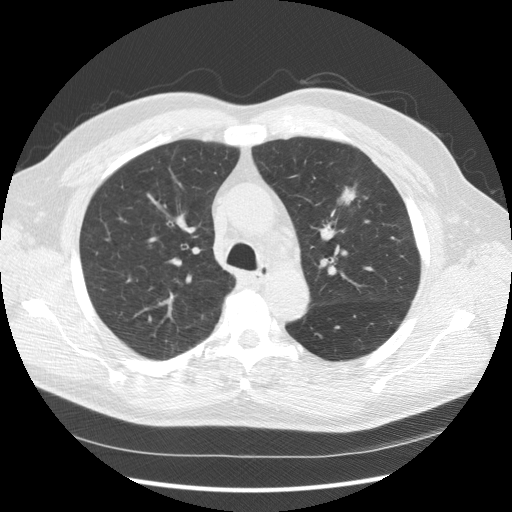
Low-dose screening chest CT, axial slice, second annual screen, lung window (W 1500 / L -600 HU), 2.5 mm slice thickness, standard (soft-tissue) reconstruction kernel (STANDARD), 120 kVp. Male, age 65 years at enrolment.
Lesion marked by an expert reader, bounding box <327,174,374,223> (left, top, right, bottom; pixels). The screening reader recorded 2 non-calcified nodules or masses ≥4 mm on this exam (left upper lobe, right upper lobe); which of them this box marks is not recorded. Later outcome: lung cancer diagnosed 120 days after this screen — carcinoma, NOS, left upper lobe, poorly differentiated (G3), stage IIIA (AJCC 6th edition), 25 mm at pathology.